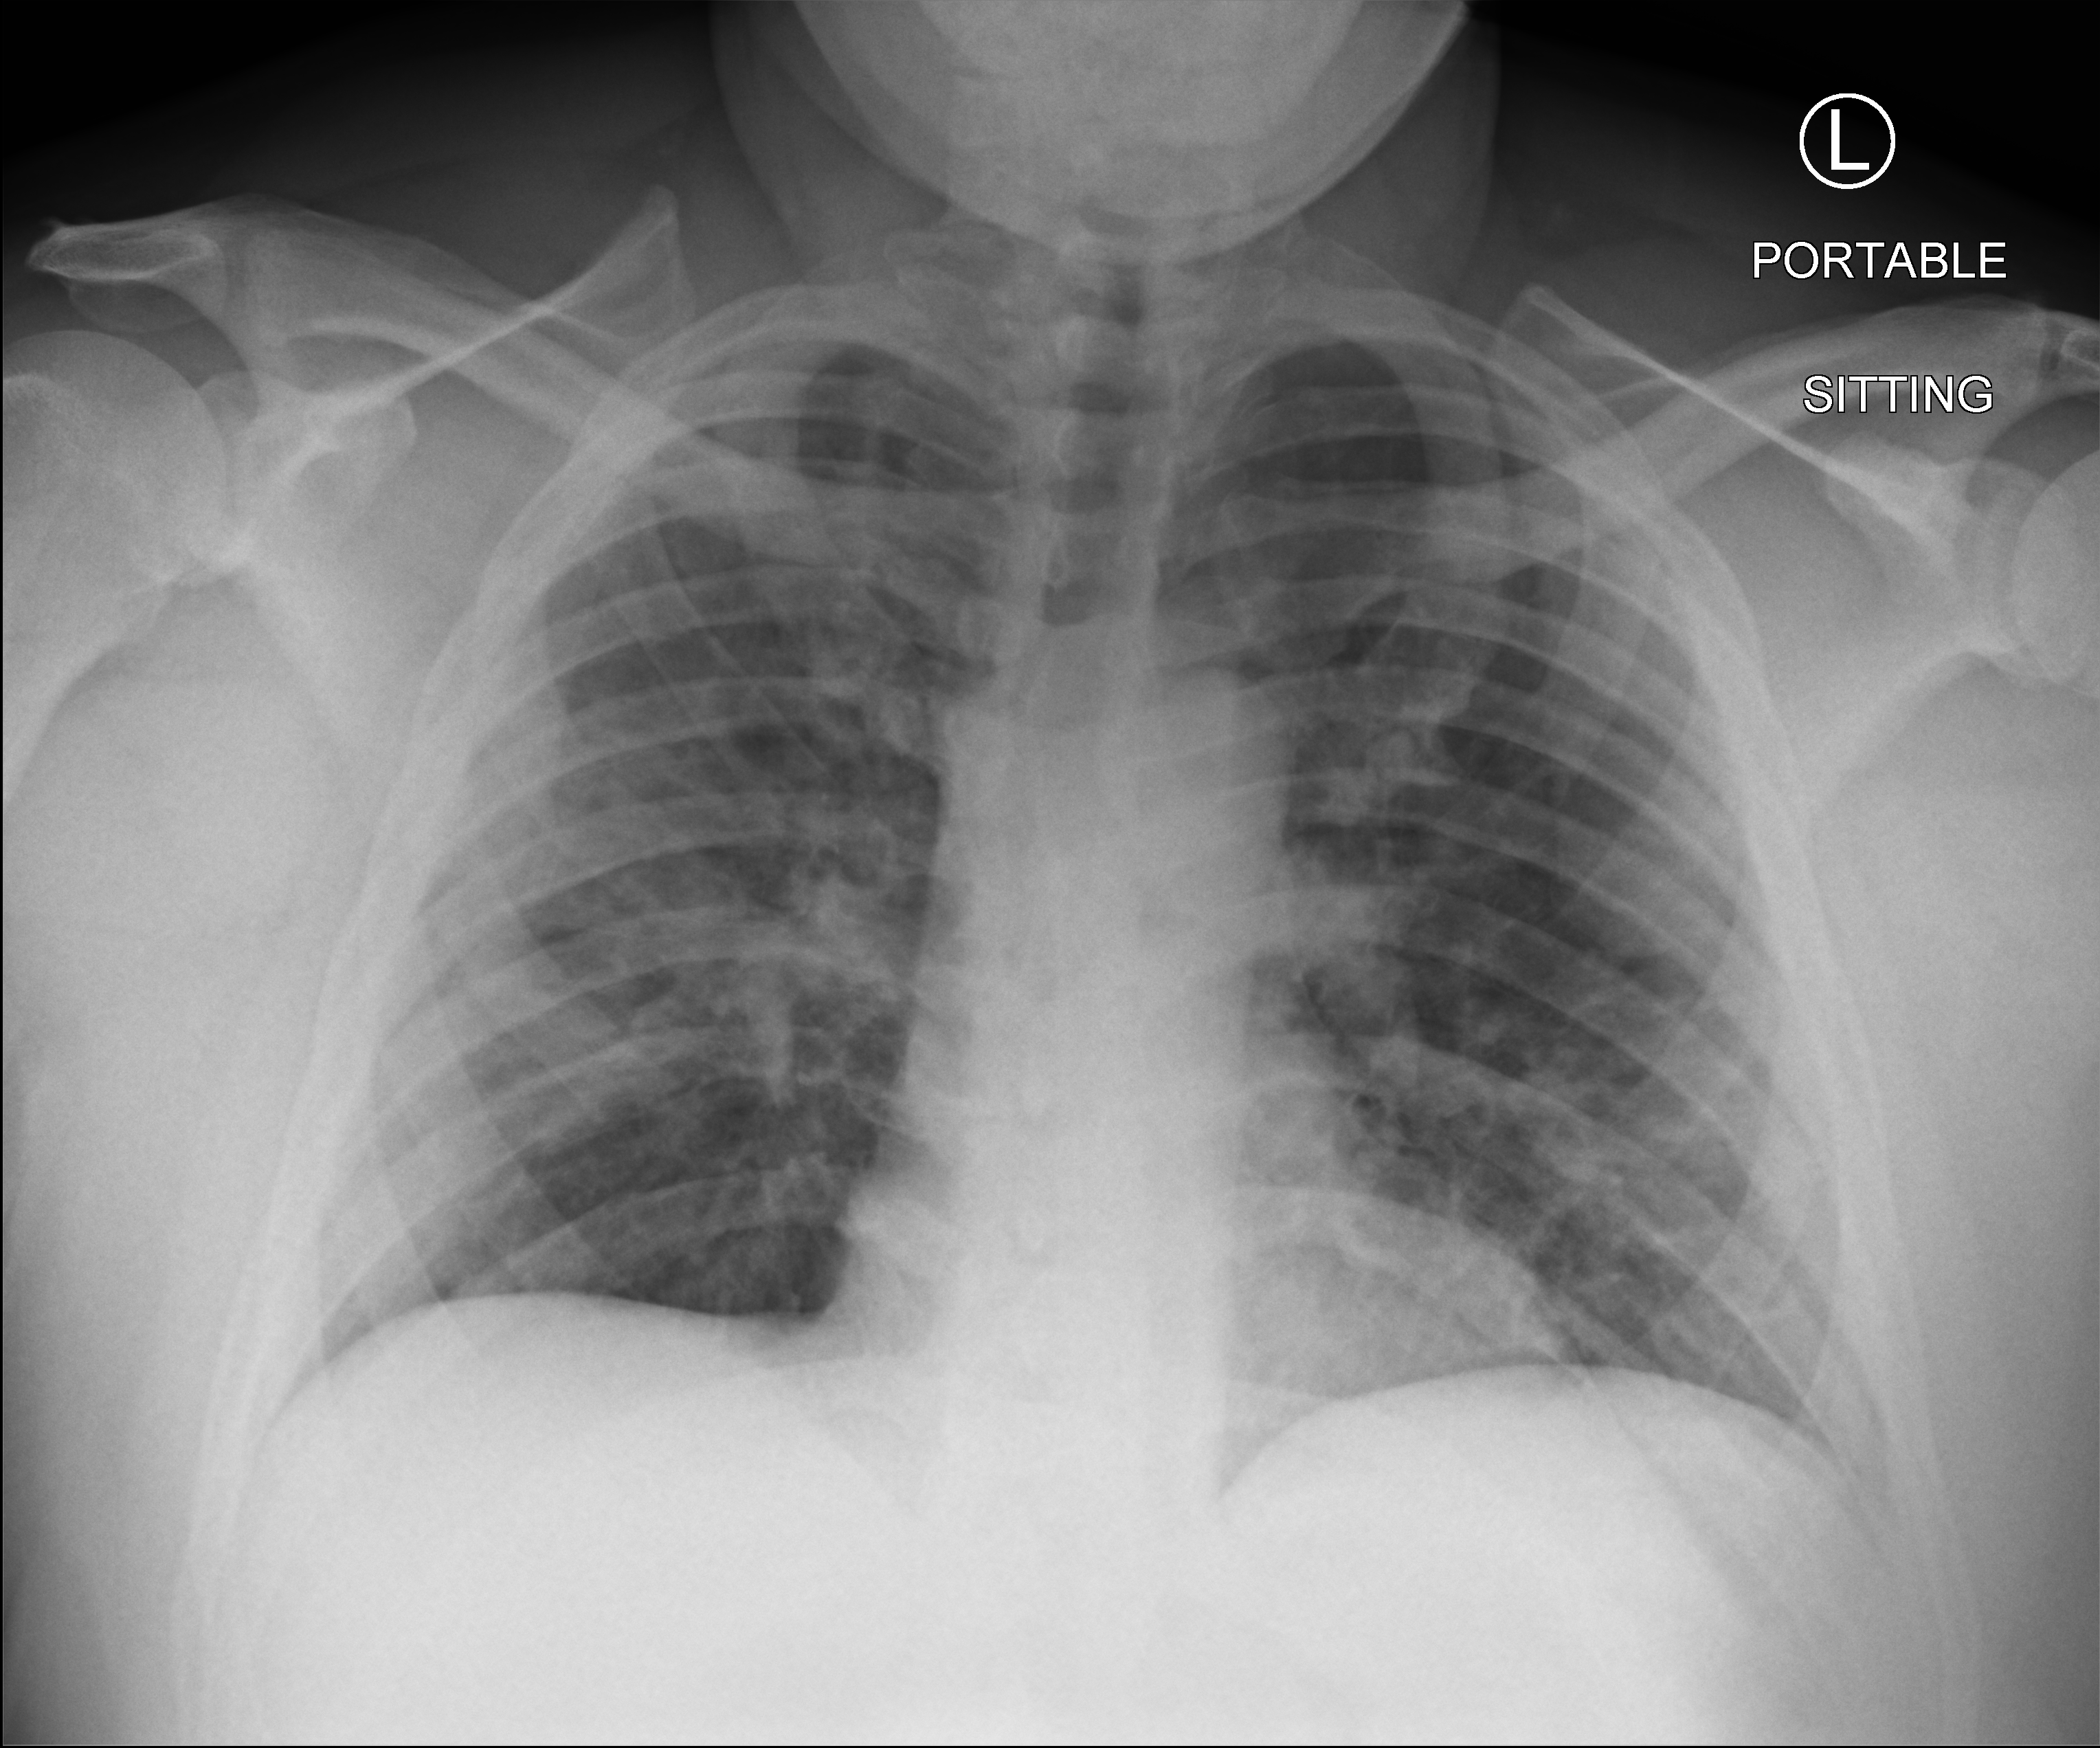
Bedside chest radiograph (computed radiography), anteroposterior (AP) projection. Patient hospitalised with COVID-19; male, aged 18–59 years.
Hospital-stay facts (about this admission, not read from this image; timing relative to this image not recorded): mechanically ventilated during this hospital stay: no.